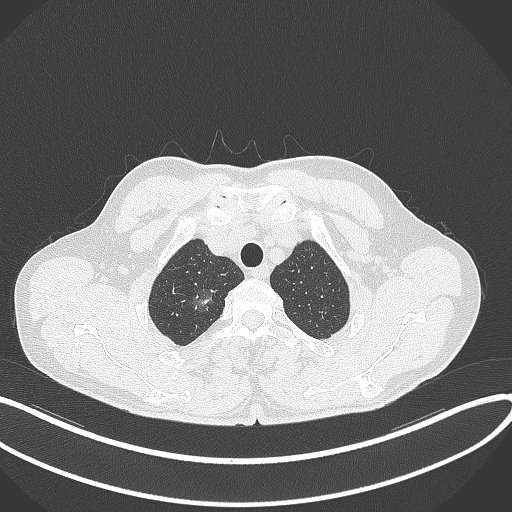
Chest CT, one axial slice. Slice 336 of 407 in the series (ordered by position). Reconstruction kernel B70f. Lung window (W 1500 / L -600 HU). 1 mm slice thickness. 512 × 512 image matrix. Patient: male, 58 years. From the clinical record (not read from this slice): clinical TNM (as recorded): T1c N0 M0; histopathological grade: G1-2.
Annotated regions visible in this slice (bounding box drawn by a radiologist):
- lung tumour (recorded histology: adenocarcinoma): bounding box (x1, y1, x2, y2) in pixels: (190, 284, 220, 314)